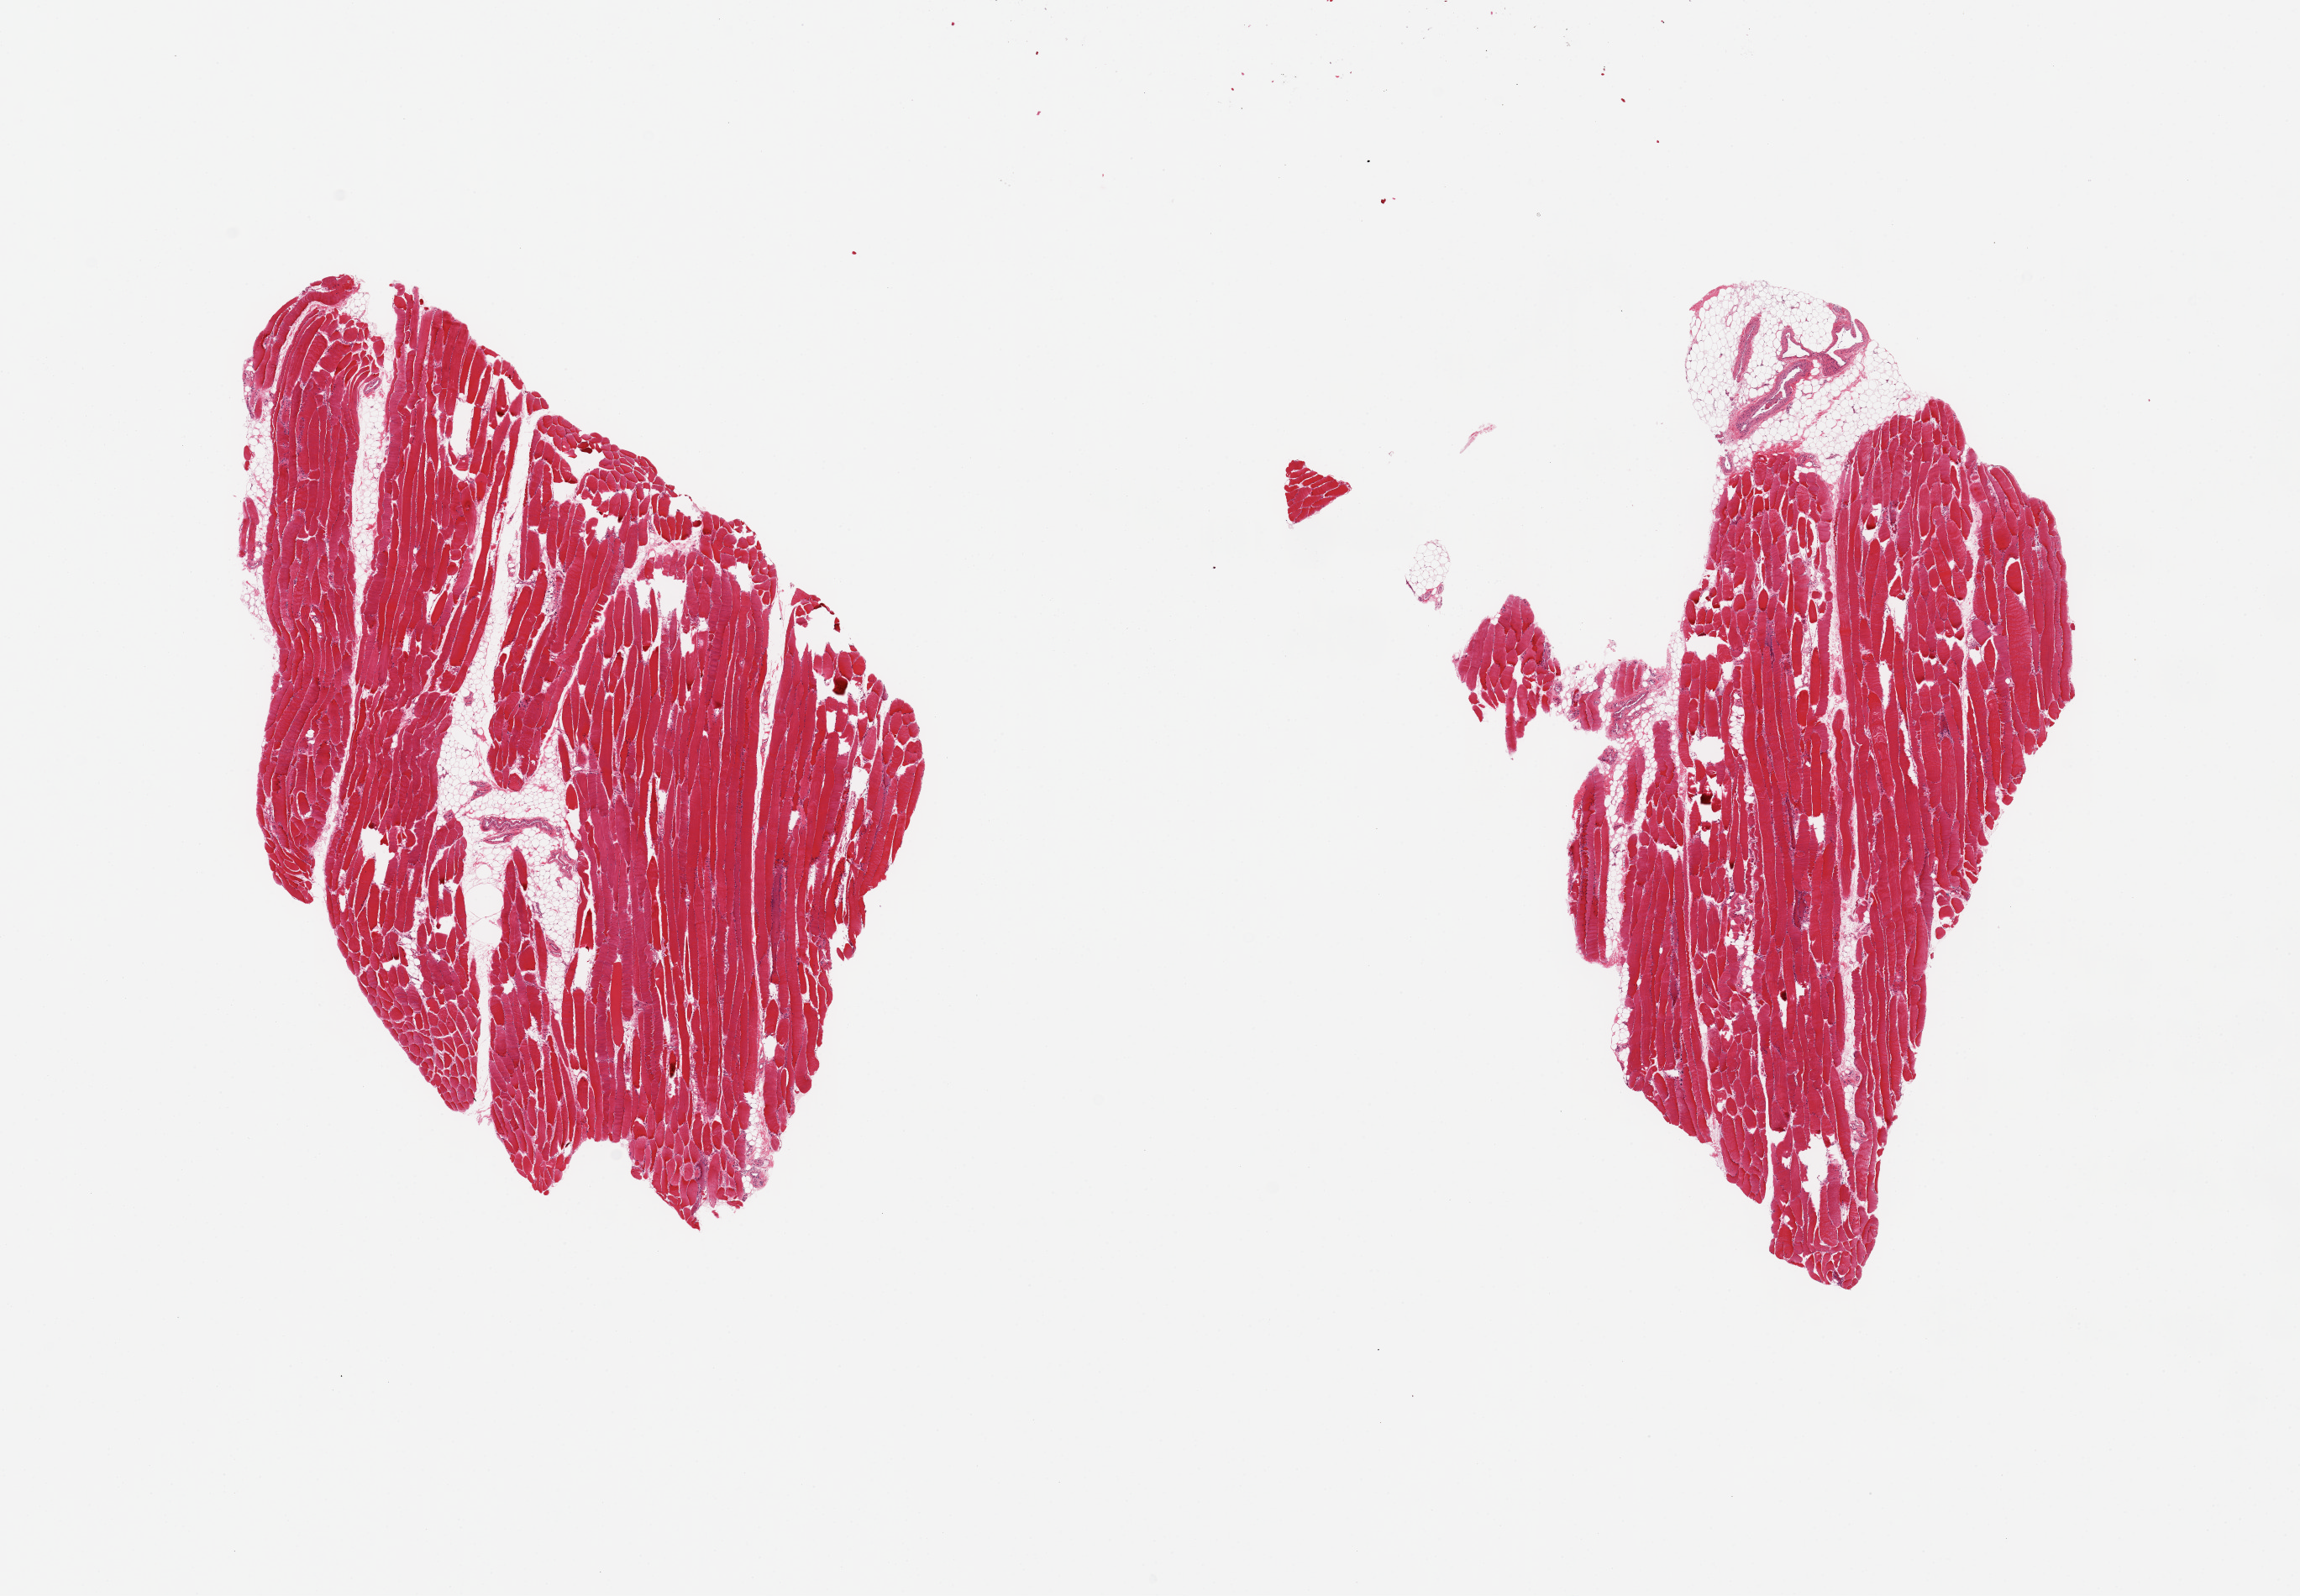
Digitized H&E-stained section, low-resolution overview of the scanned area, about 21.7 x 15.0 mm. PAXgene-fixed, paraffin-embedded tissue. Target tissue: skeletal muscle. Donor tissue sample. Donor: male.
Reviewer comment on this tissue sample: 2 pieces; 10% internal fat on 1, 10% external fat on other.